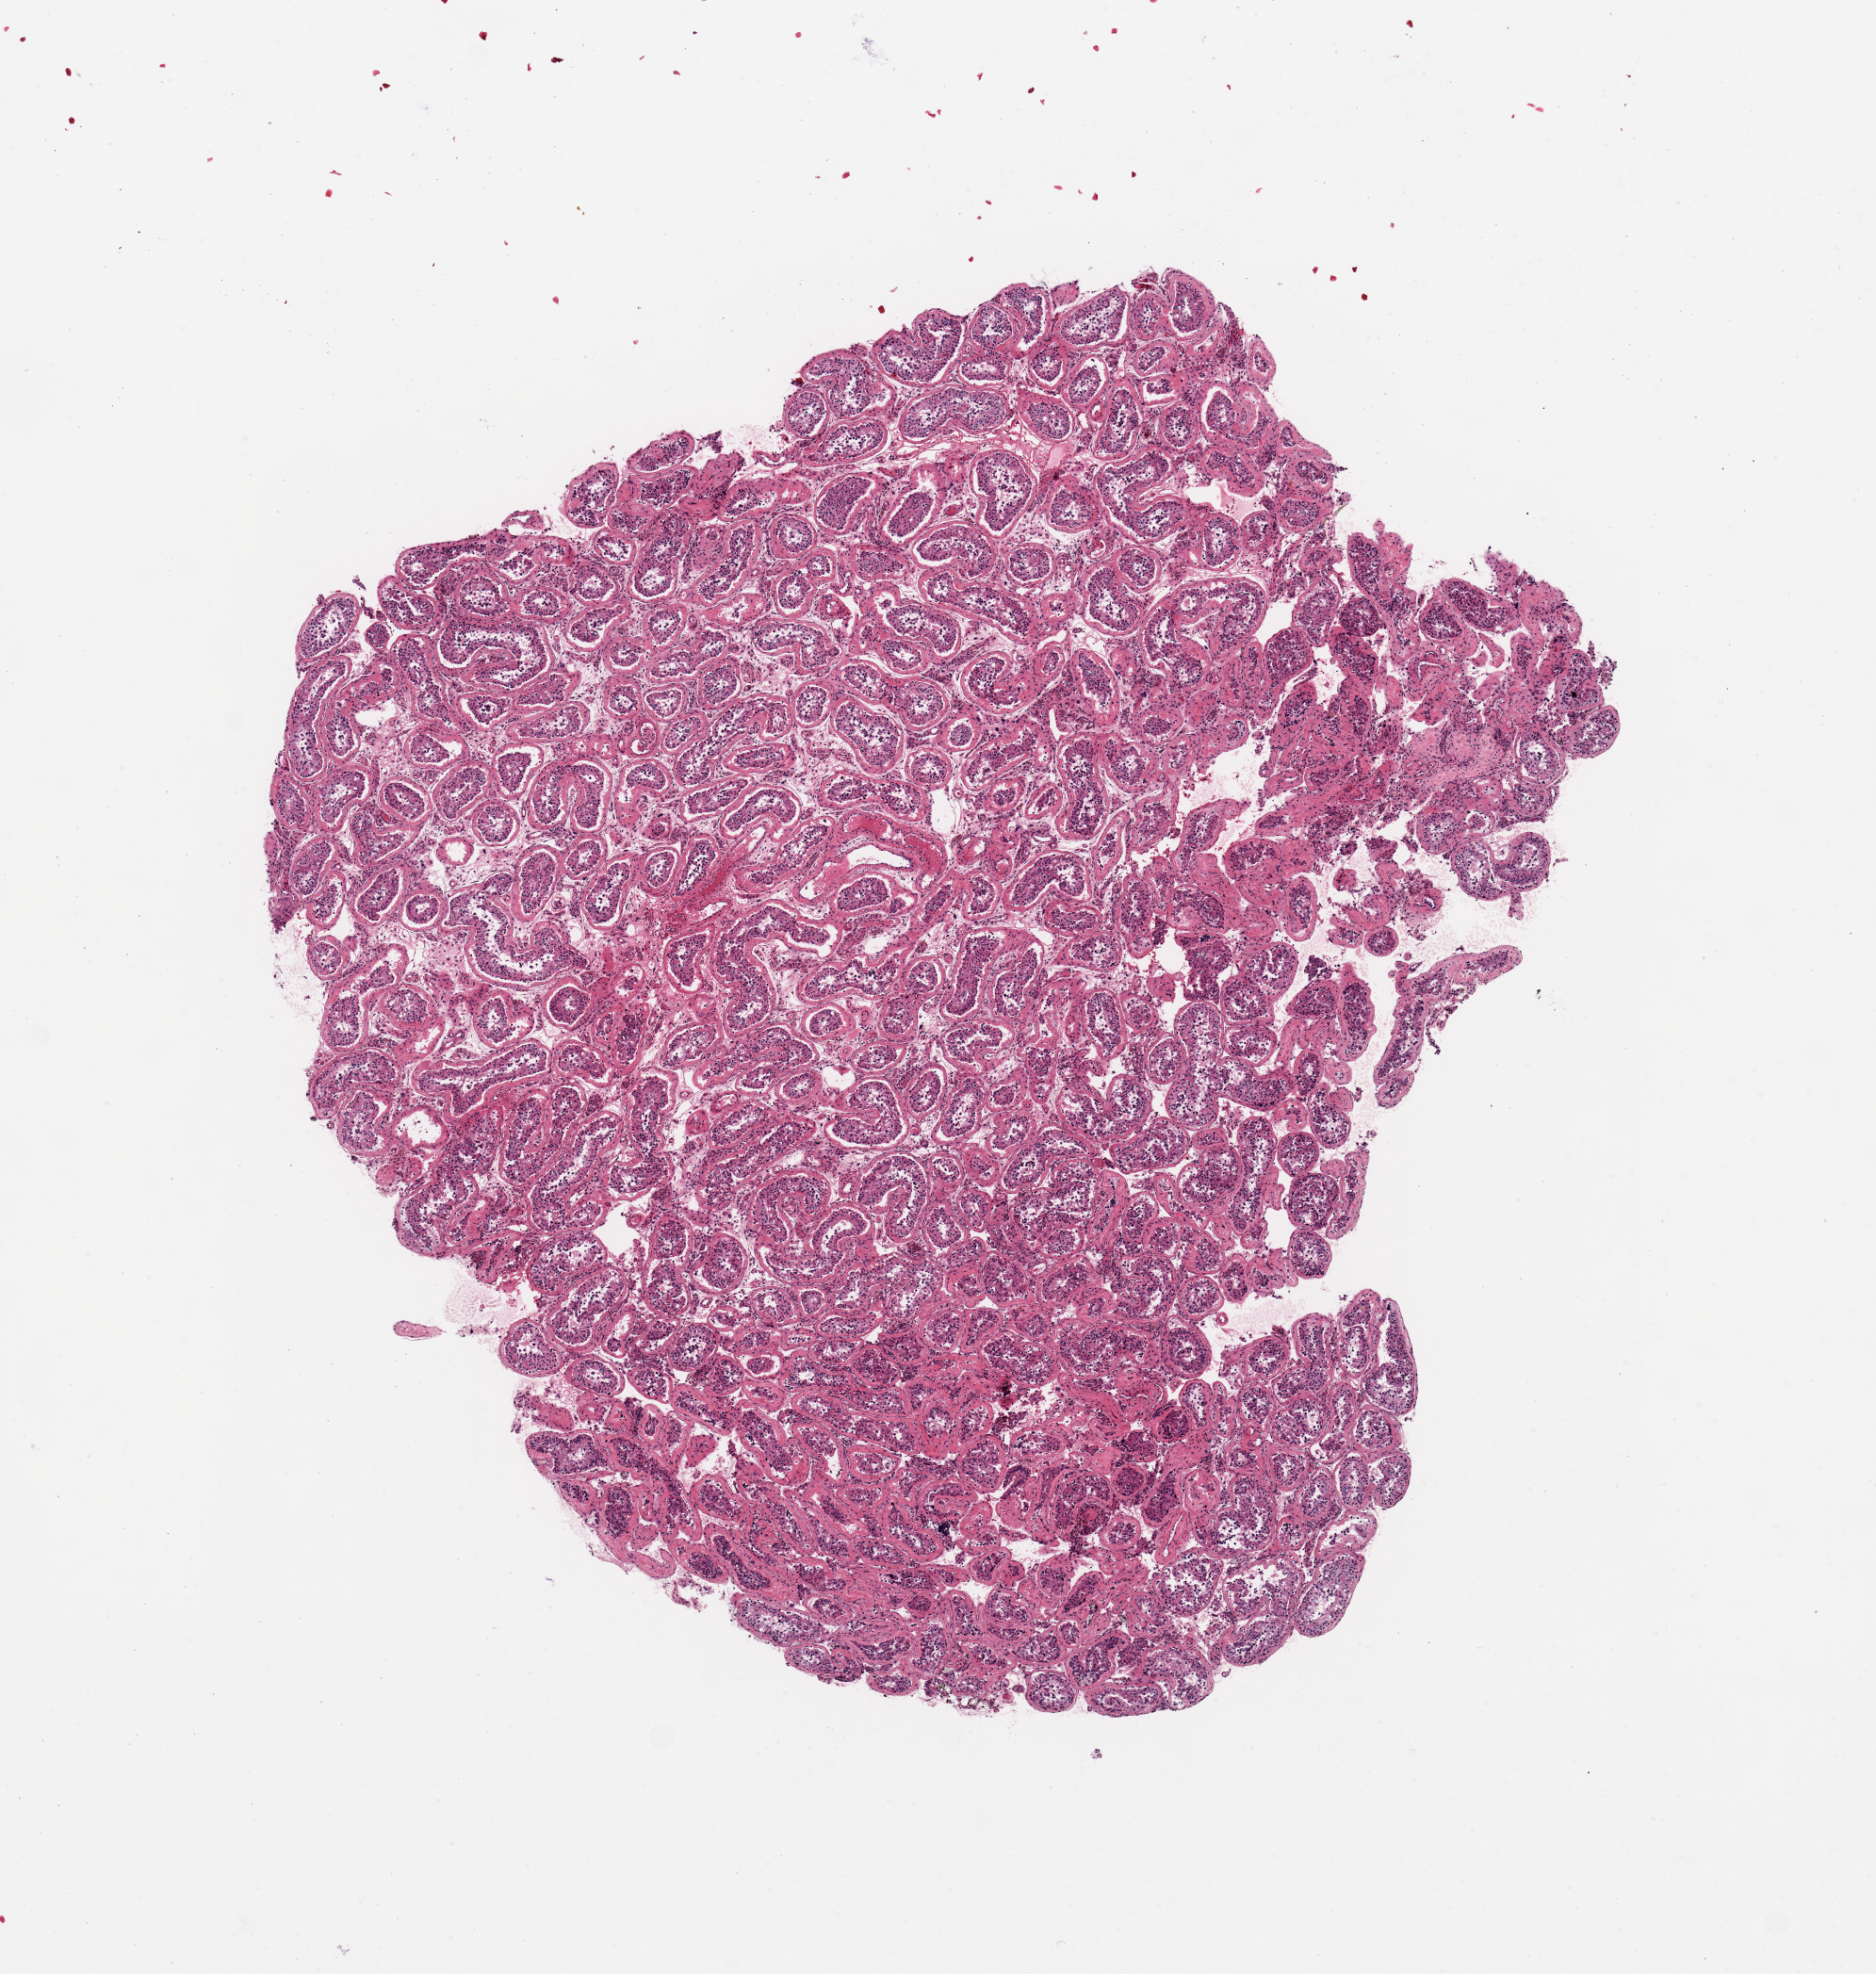
Whole-slide image, hematoxylin and eosin (H&E) stain, a low-resolution overview of the entire scanned area, about 7.9 x 8.3 mm (slide scanned at 20x); PAXgene-fixed, paraffin-embedded tissue; section of testis (target tissue); tissue donor sample. Male donor.
Reviewer comment on this tissue sample: 6x5mm.